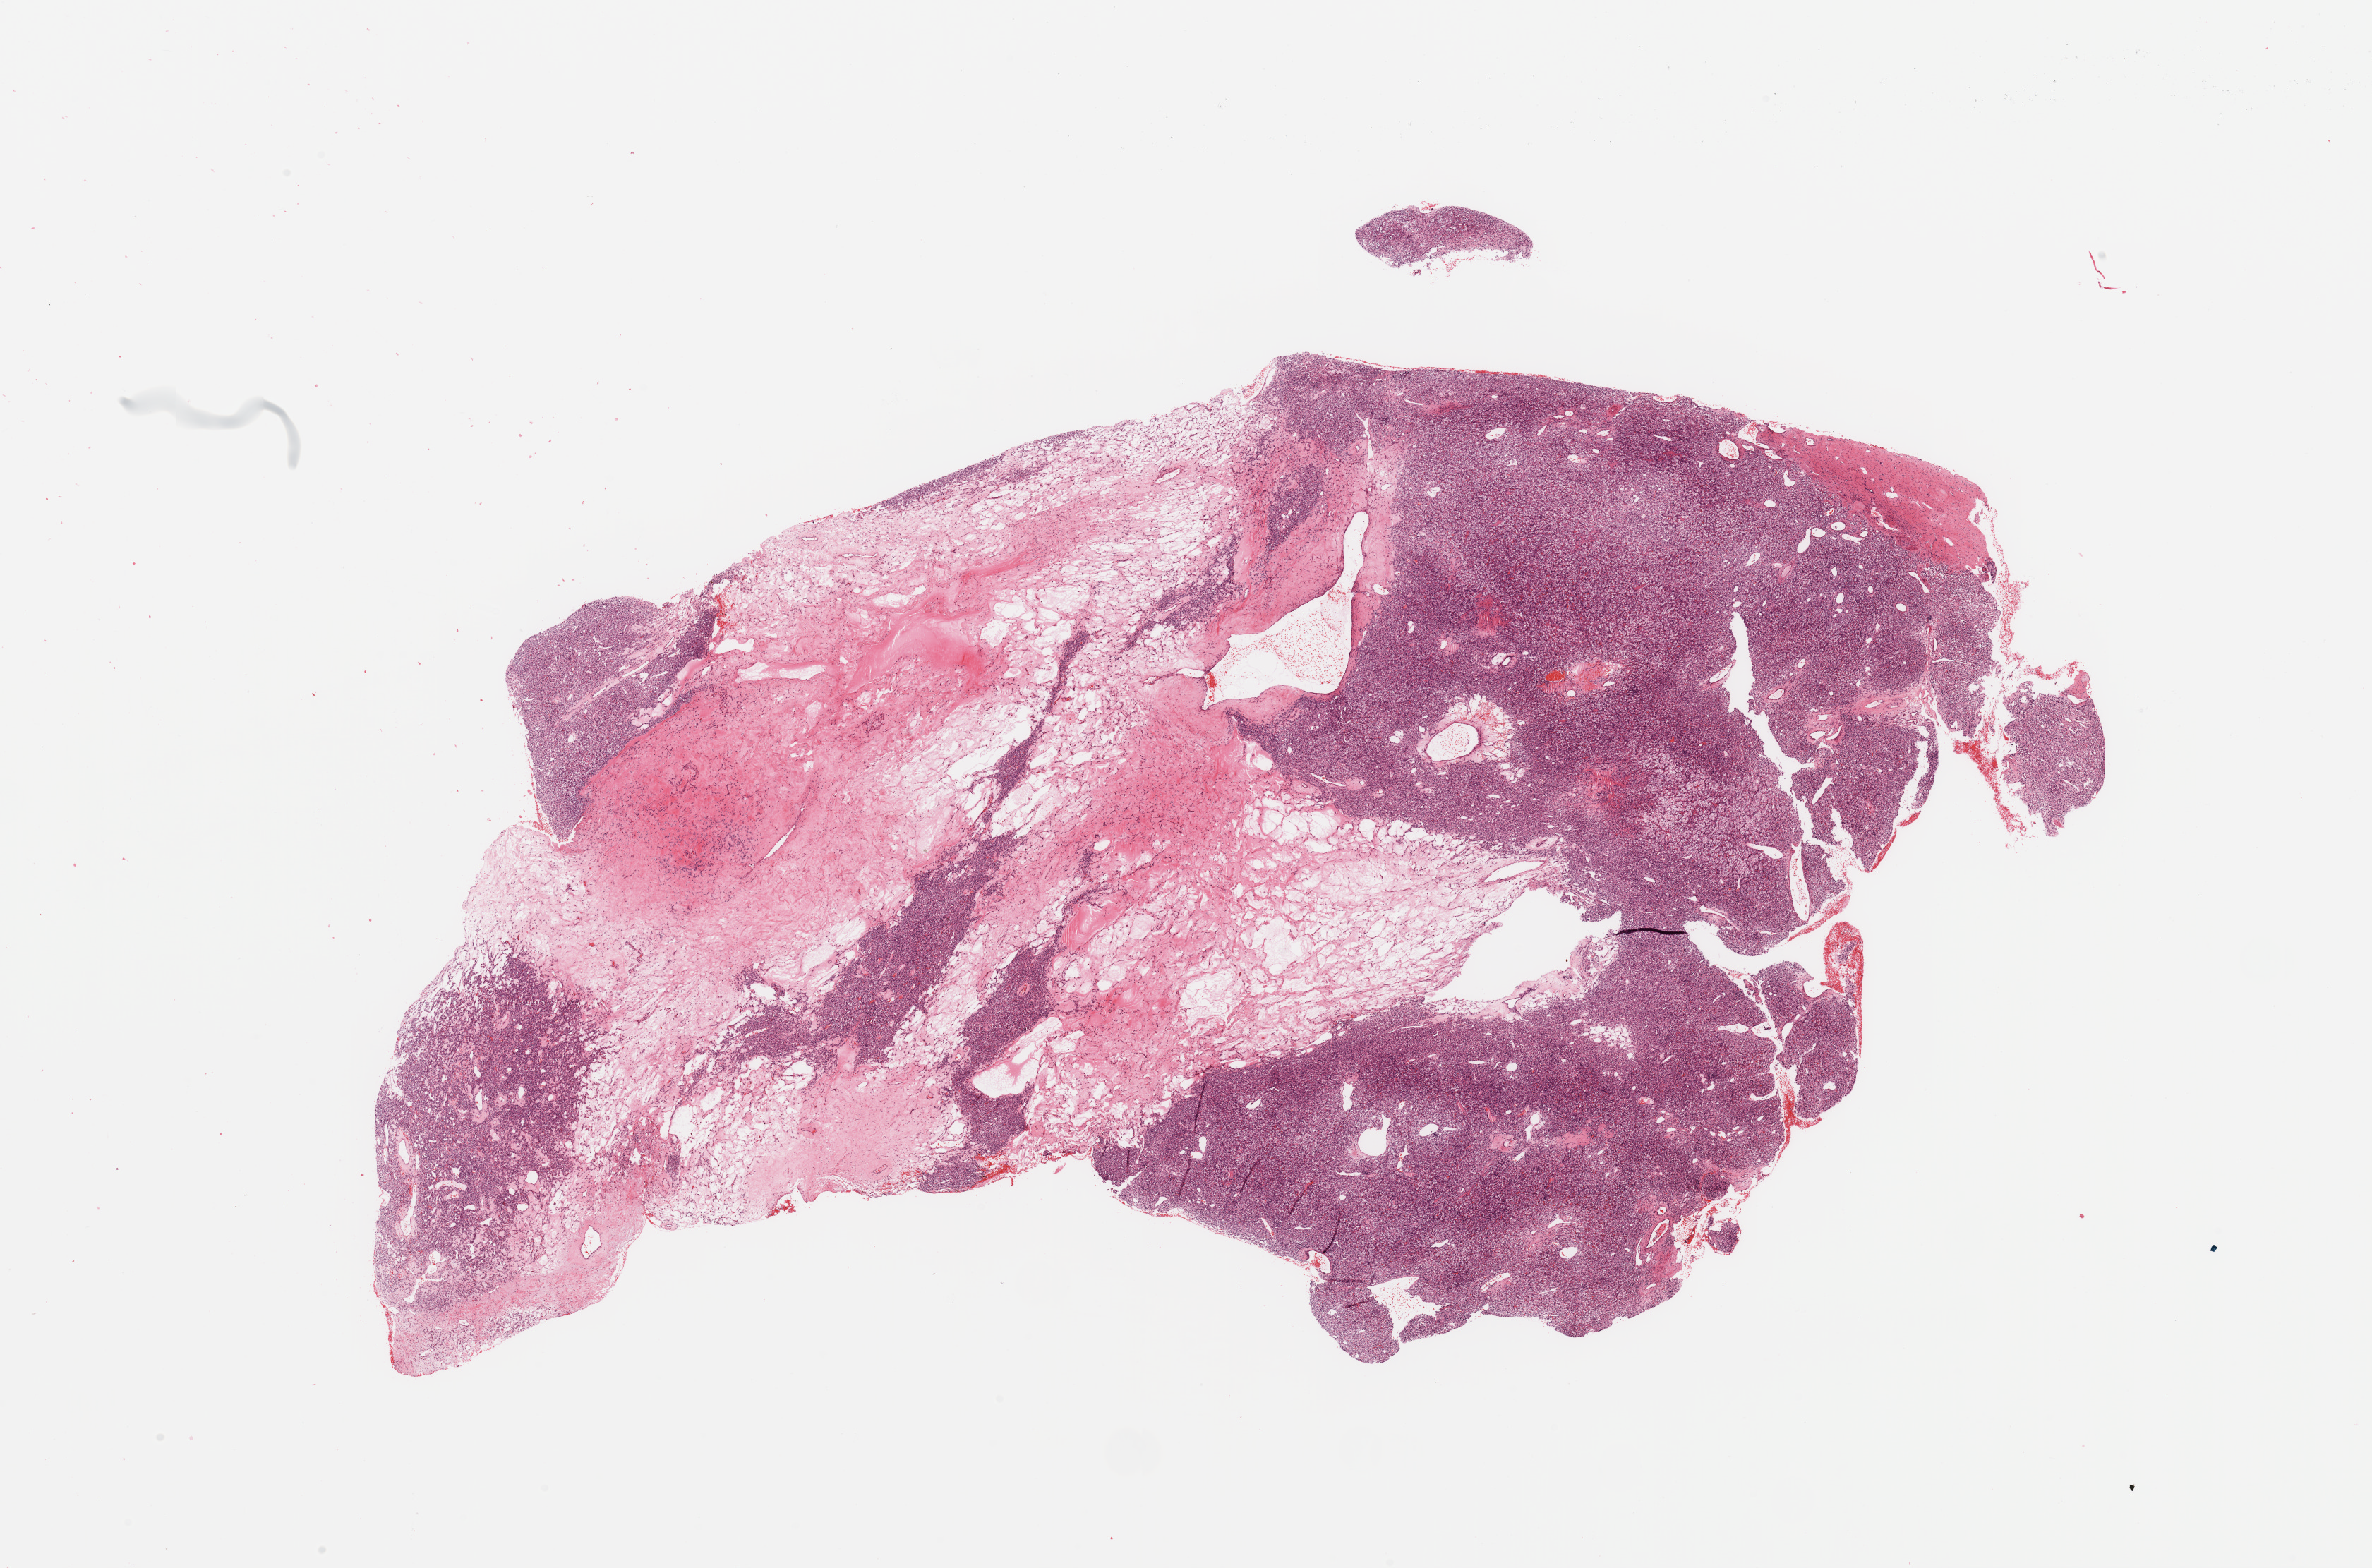
Whole-slide histology image, Hematoxylin and eosin (H&E) stained — a low-resolution overview of the entire scanned area, about 26.6 x 17.6 mm (slide scanned at 20x). Kidney, tumour tissue. Male, 63 y/o.
Diagnosis: Renal cell carcinoma, NOS.